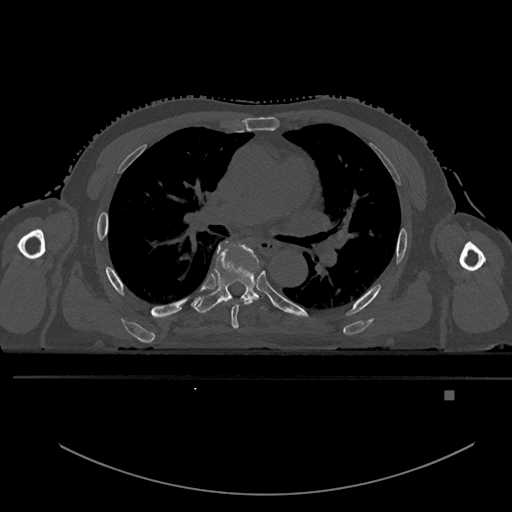
CT including the spine, one axial slice. Position 328 of 969 along the scan axis. Bone window (W 1800 / L 400 HU). 0.5 mm slice thickness. 512 × 512 image matrix. Male patient, age 82 years. From the clinical record (not read from this slice): primary cancer: prostate.
Structures marked on this image (semi-automatic segmentation, software-assisted and operator-edited):
- T5 vertebra: bounding box [x1, y1, x2, y2] px = [224, 241, 260, 329]
- T6 vertebra: [191, 242, 266, 314]